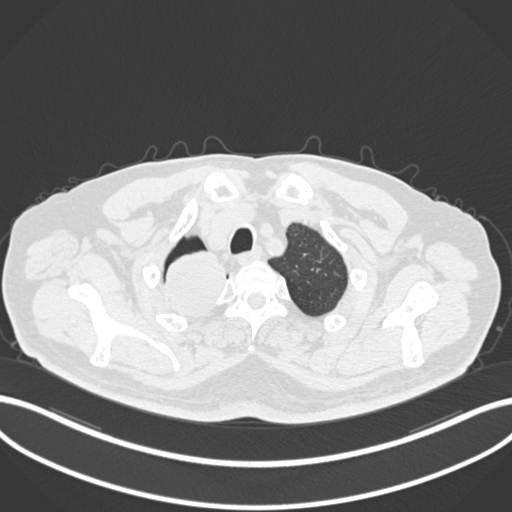
Chest CT, one axial slice. Slice 190 of 218 in the series (ordered by position). Reconstruction kernel B30f. Lung window (W 1500 / L -600 HU). 1 mm slice thickness. 512 × 512 image matrix. Patient: male, 68 years. From the clinical record (not read from this slice): clinical TNM (as recorded): T2a N0 M0.
Structures marked on this image (bounding box drawn by a radiologist):
- lung tumour (recorded histology: adenocarcinoma): bounding box [x1, y1, x2, y2] px = [160, 247, 235, 326]